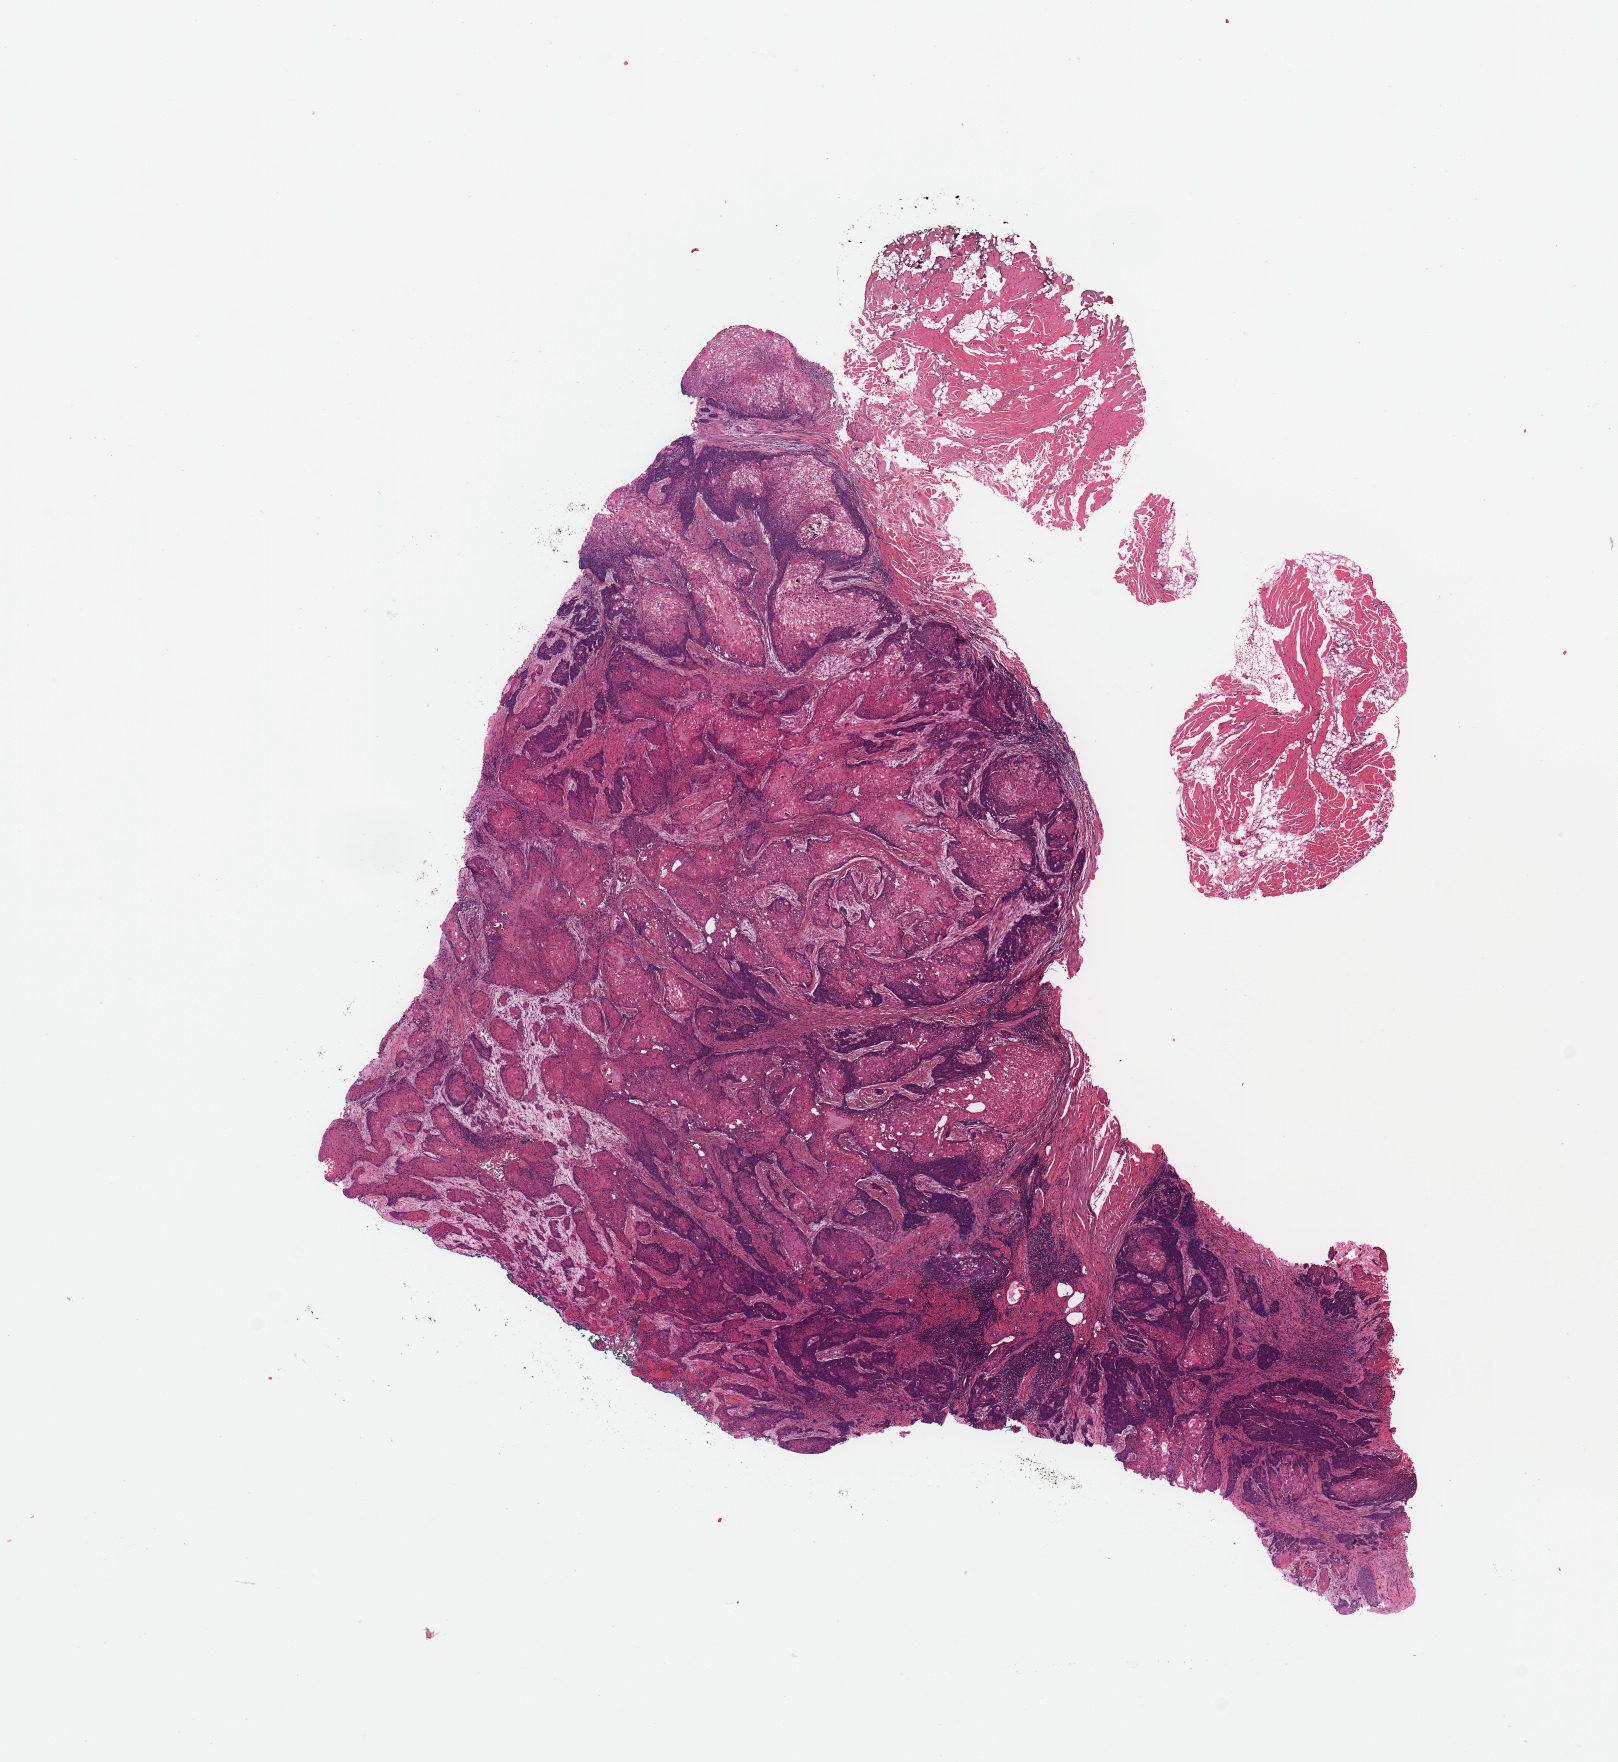
Whole-slide histology image, H&E — low-resolution overview of the scanned area, about 12.8 x 13.9 mm; tumour tissue sample, sampled site: tongue. Male, 61 y/o. Histologic grade: G2 (moderately differentiated). Composition of this section per pathologist review: tumour nuclei 80%, necrosis 5%.
• AJCC pathologic stage: III
• diagnosis: Squamous cell carcinoma, NOS (tongue, NOS)
• primary tumour site (as recorded): oral cavity